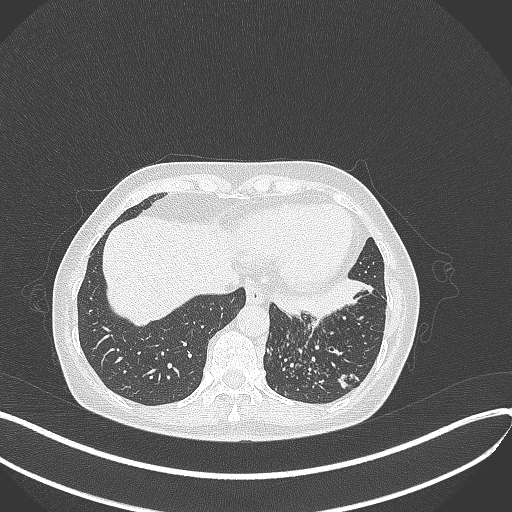
Chest CT, one axial slice. Position 101 of 429 along the scan axis. Lung window (W 1500 / L -600 HU). 1 mm slice thickness. 512 × 512 image matrix, field of view 400 × 400 mm. Patient: female, 63 years. Case-level facts recorded for this patient, not image findings: clinical TNM (as recorded): T1b N0 M0.
Annotated regions visible in this slice (rectangle marked by the reading radiologist):
- lung tumour (recorded histology: adenocarcinoma): bounding box [x1, y1, x2, y2] px = [271, 274, 378, 327]